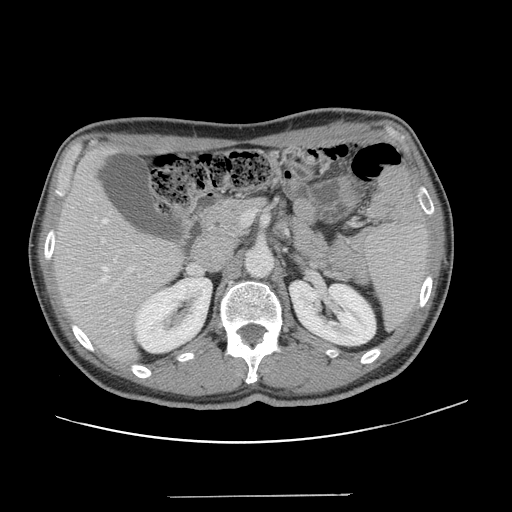
Contrast-enhanced abdominal CT, one axial slice. Position 75 of 131 along the scan axis. Intravenous contrast given. Soft-tissue window (W 400 / L 40 HU). 512 × 512 image matrix, field of view 403 × 403 mm. Male patient, age 60 years. Case-level facts recorded for this patient, not image findings: diagnosis: colorectal cancer liver metastases, imaged before liver resection; multiple liver metastases: no; largest metastasis: 2.5 cm; disease in both lobes: no.
Outlined on this slice (outlined manually by an expert reader):
- hepatic veins: bounding box <102,219,116,282> (left, top, right, bottom; pixels)
- liver: <55,150,182,361>
- planned liver remnant (the part of the liver to remain after resection): <54,150,182,360>